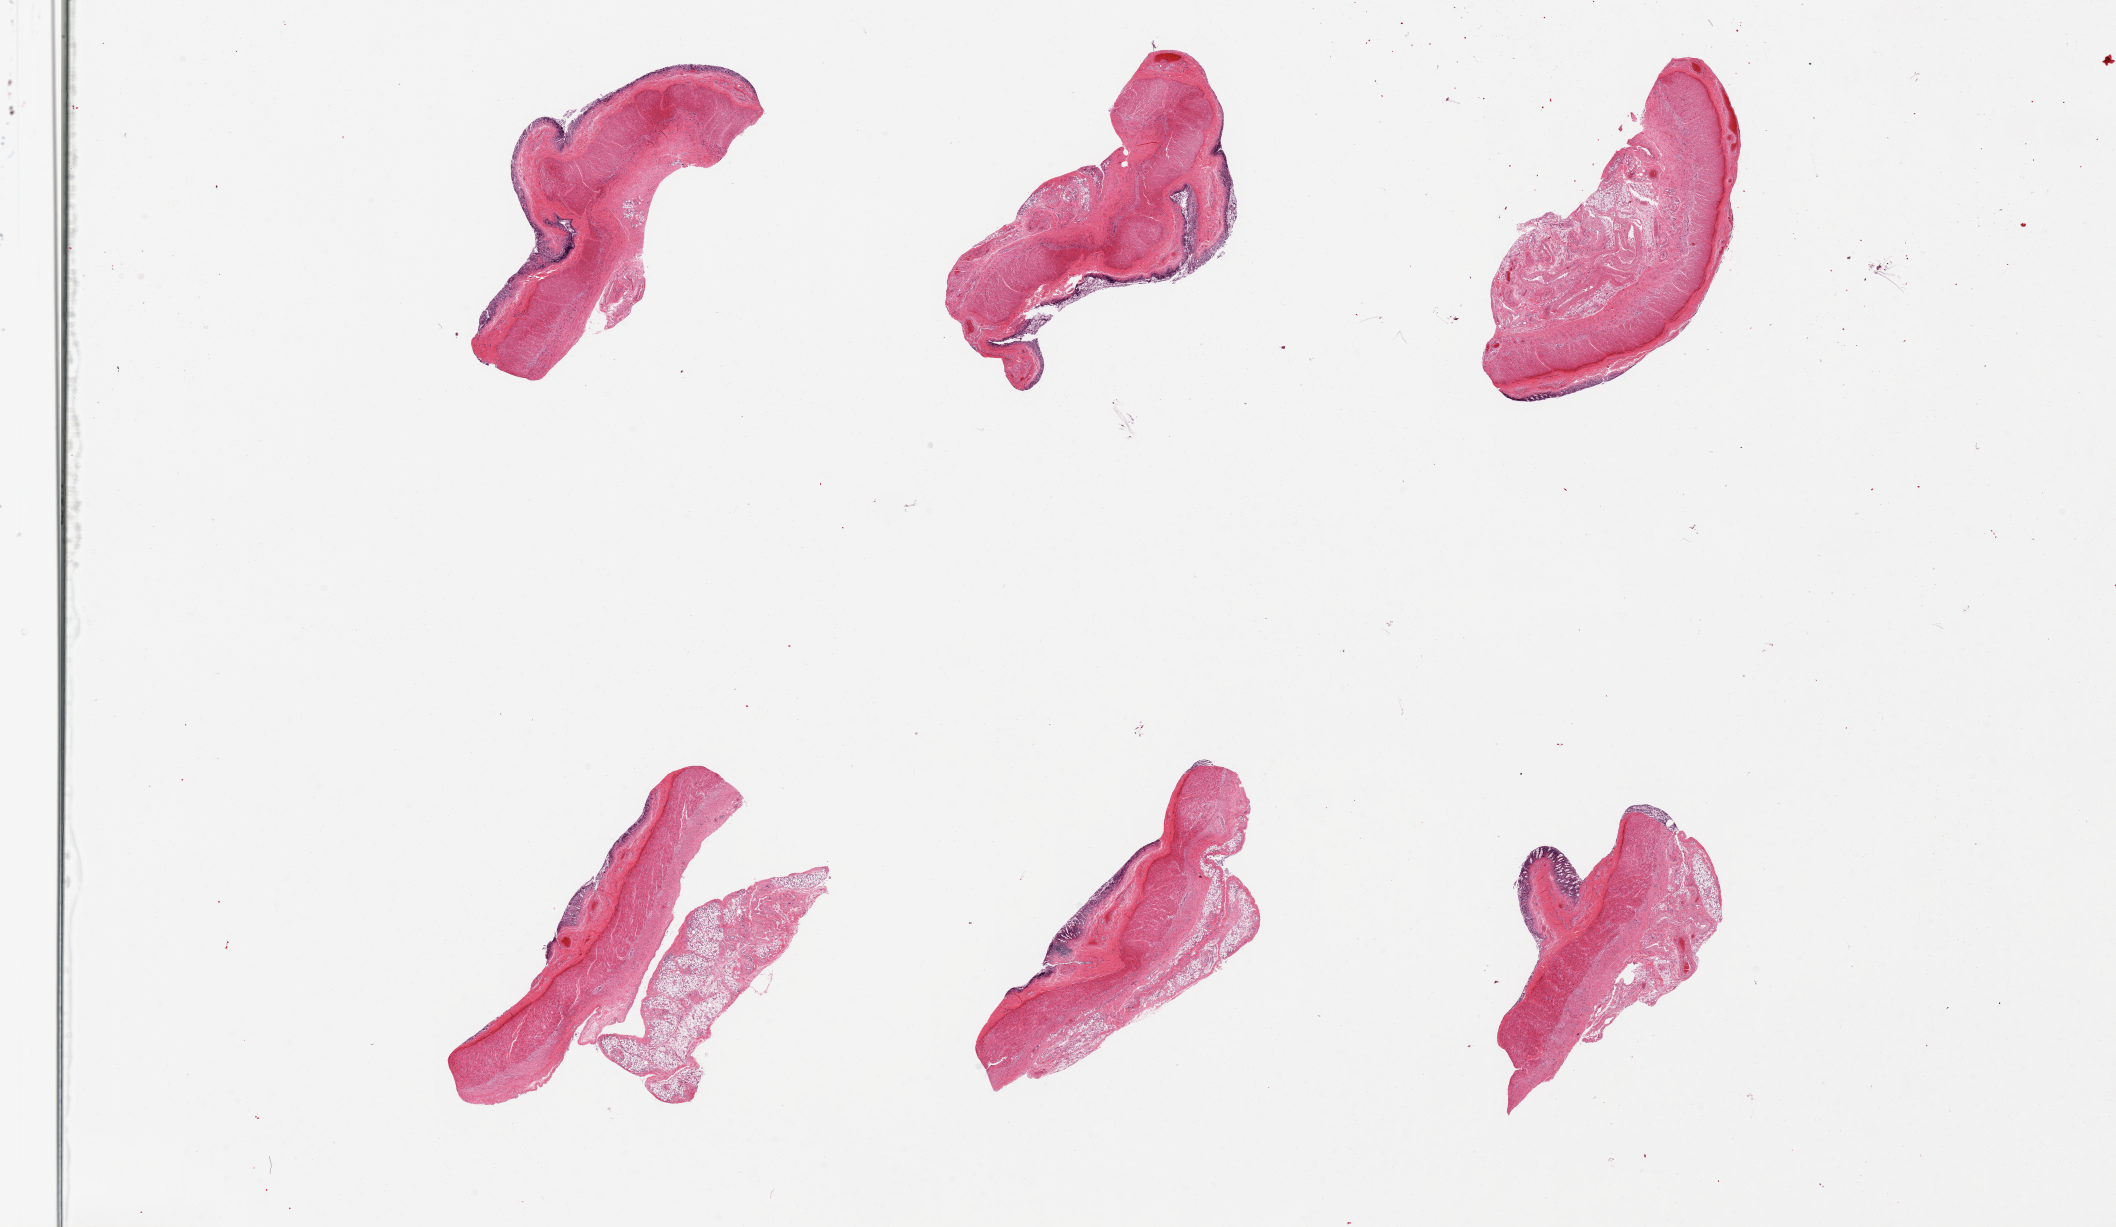
Digitized H&E-stained section — whole scanned area (about 33.5 x 19.4 mm, from a 20x scan) shown as a low-resolution overview; PAXgene-fixed paraffin-embedded (PFPE) section; section of transverse colon (target tissue); donor tissue sample. Male donor.
• pathologist's review note for this sample: 6 pieces, mucosa totally autolyzed and /or sloughed